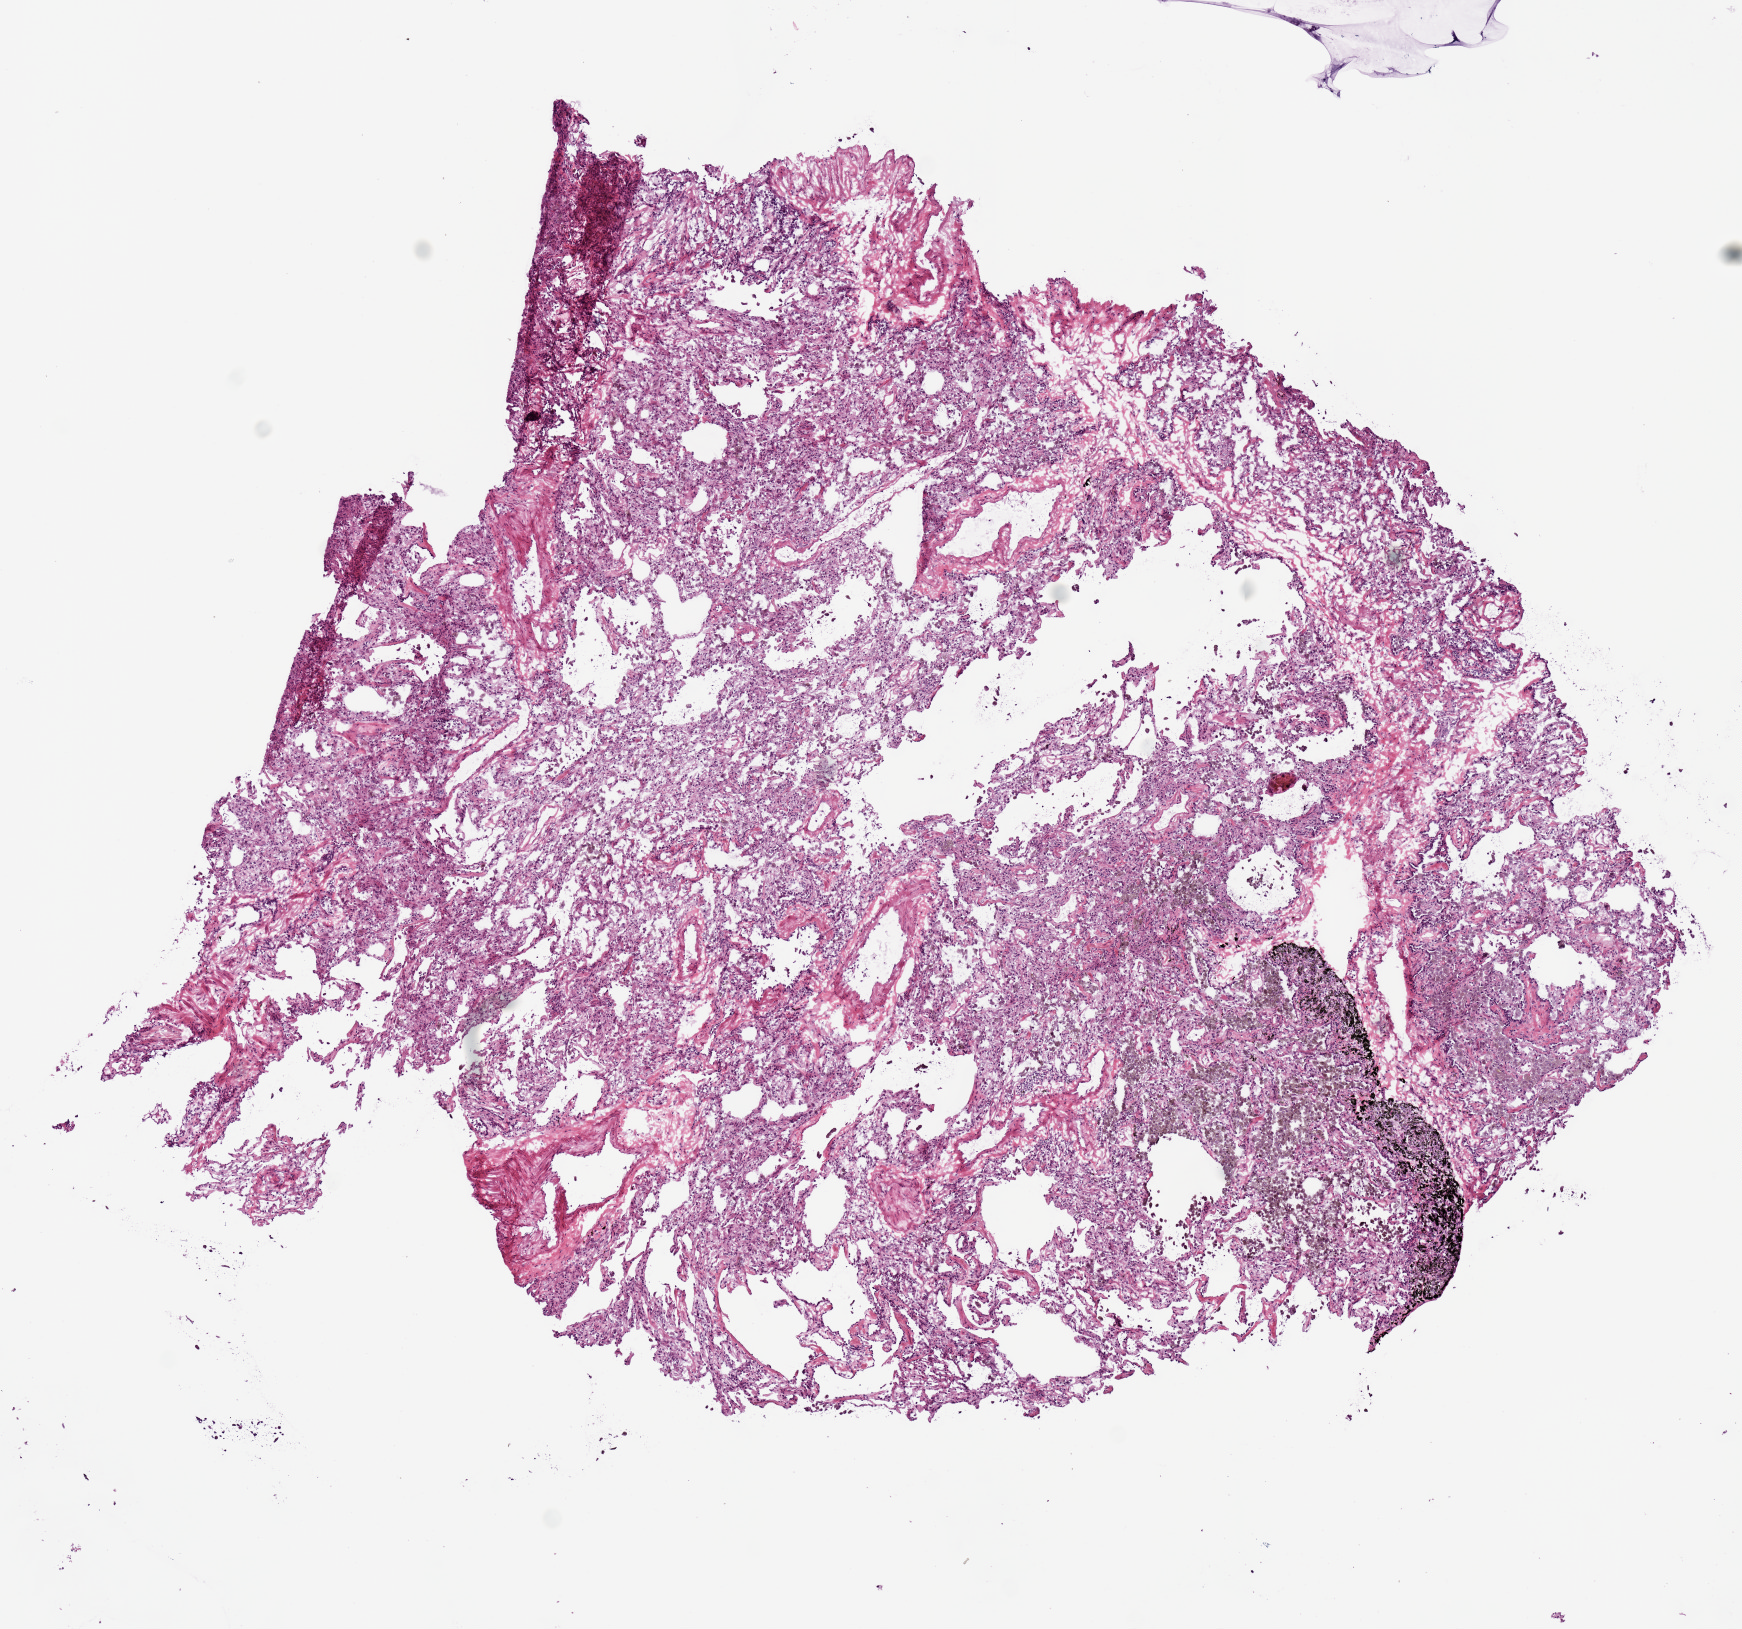
Whole-slide histology image, H&E-stained, a low-resolution overview of the entire scanned area, about 6.9 x 6.4 mm, frozen section, lung, solid tissue normal (non-tumour tissue) sample. Patient: female, age at initial diagnosis 59 years.
• this section: solid tissue normal (non-tumour) sample from the same patient
• patient diagnosis: Adenocarcinoma, NOS (lower lobe, lung)